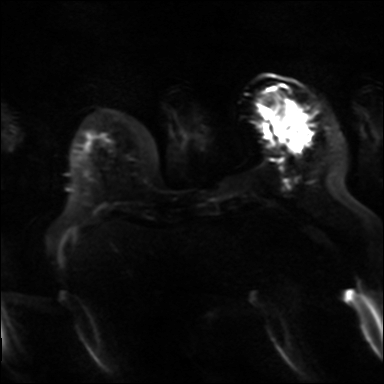
Breast MRI, one axial slice; diffusion-weighted series; image 2 of 4 stored at this slice position (different b-values; order by instance number); 3 T; 384 × 384 image matrix, field of view 320 × 320 mm. Female patient.
Annotated regions visible in this slice (outlined manually by an expert reader):
- tumour on diffusion-weighted imaging: bounding box (x1, y1, x2, y2) in pixels: (290, 124, 306, 143)